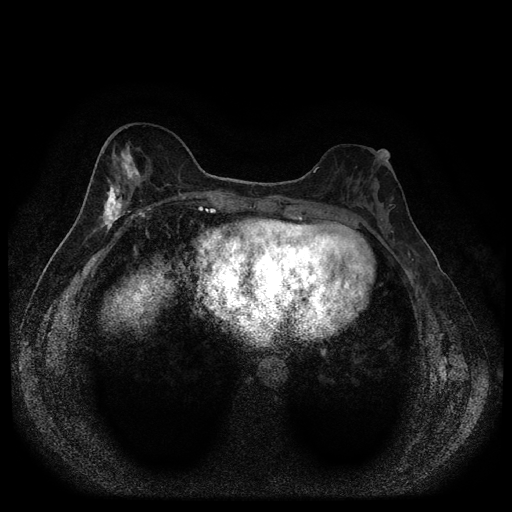
Breast MRI (dynamic contrast-enhanced, multi-phase), one axial slice. Slice 40 of 116 in the series (ordered by position). Dynamic contrast-enhanced series, time point 2 of 5 at this slice position (early post-contrast). 1.5 T. TE 2.7 ms, TR 5.4 ms. 512 × 512 image matrix, field of view 330 × 330 mm. Patient: female, 49 years.
Annotated regions visible in this slice (semi-automatically segmented with operator editing):
- breast lesion (labelled 'tumour' in the annotation; benign lesions carry a separate 'benign' label): bounding box [x1, y1, x2, y2] px = [98, 141, 143, 237]